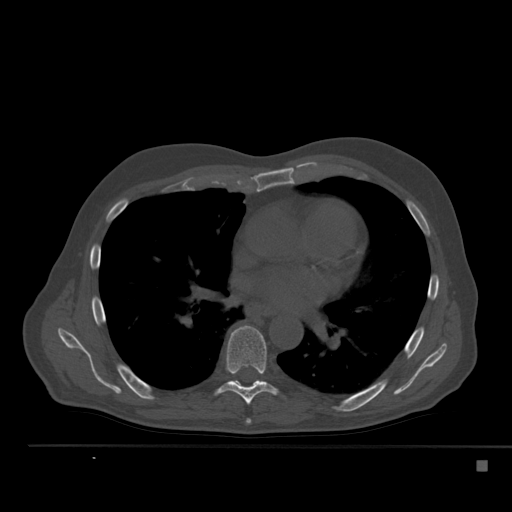
CT including the spine, one axial slice. Slice 327 of 517 in the series (ordered by position). 120 kVp. Bone window (W 1800 / L 400 HU). 1.5 mm slice thickness. 512 × 512 image matrix, field of view 408 × 408 mm. Male patient, age 70 years. Case-level facts recorded for this patient, not image findings: primary cancer: renal.
Outlined on this slice (semi-automatically segmented with operator editing):
- T6 vertebra: box from (x=246, y=419) to (x=251, y=424) px
- T7 vertebra: (x=216, y=325)–(x=278, y=405)